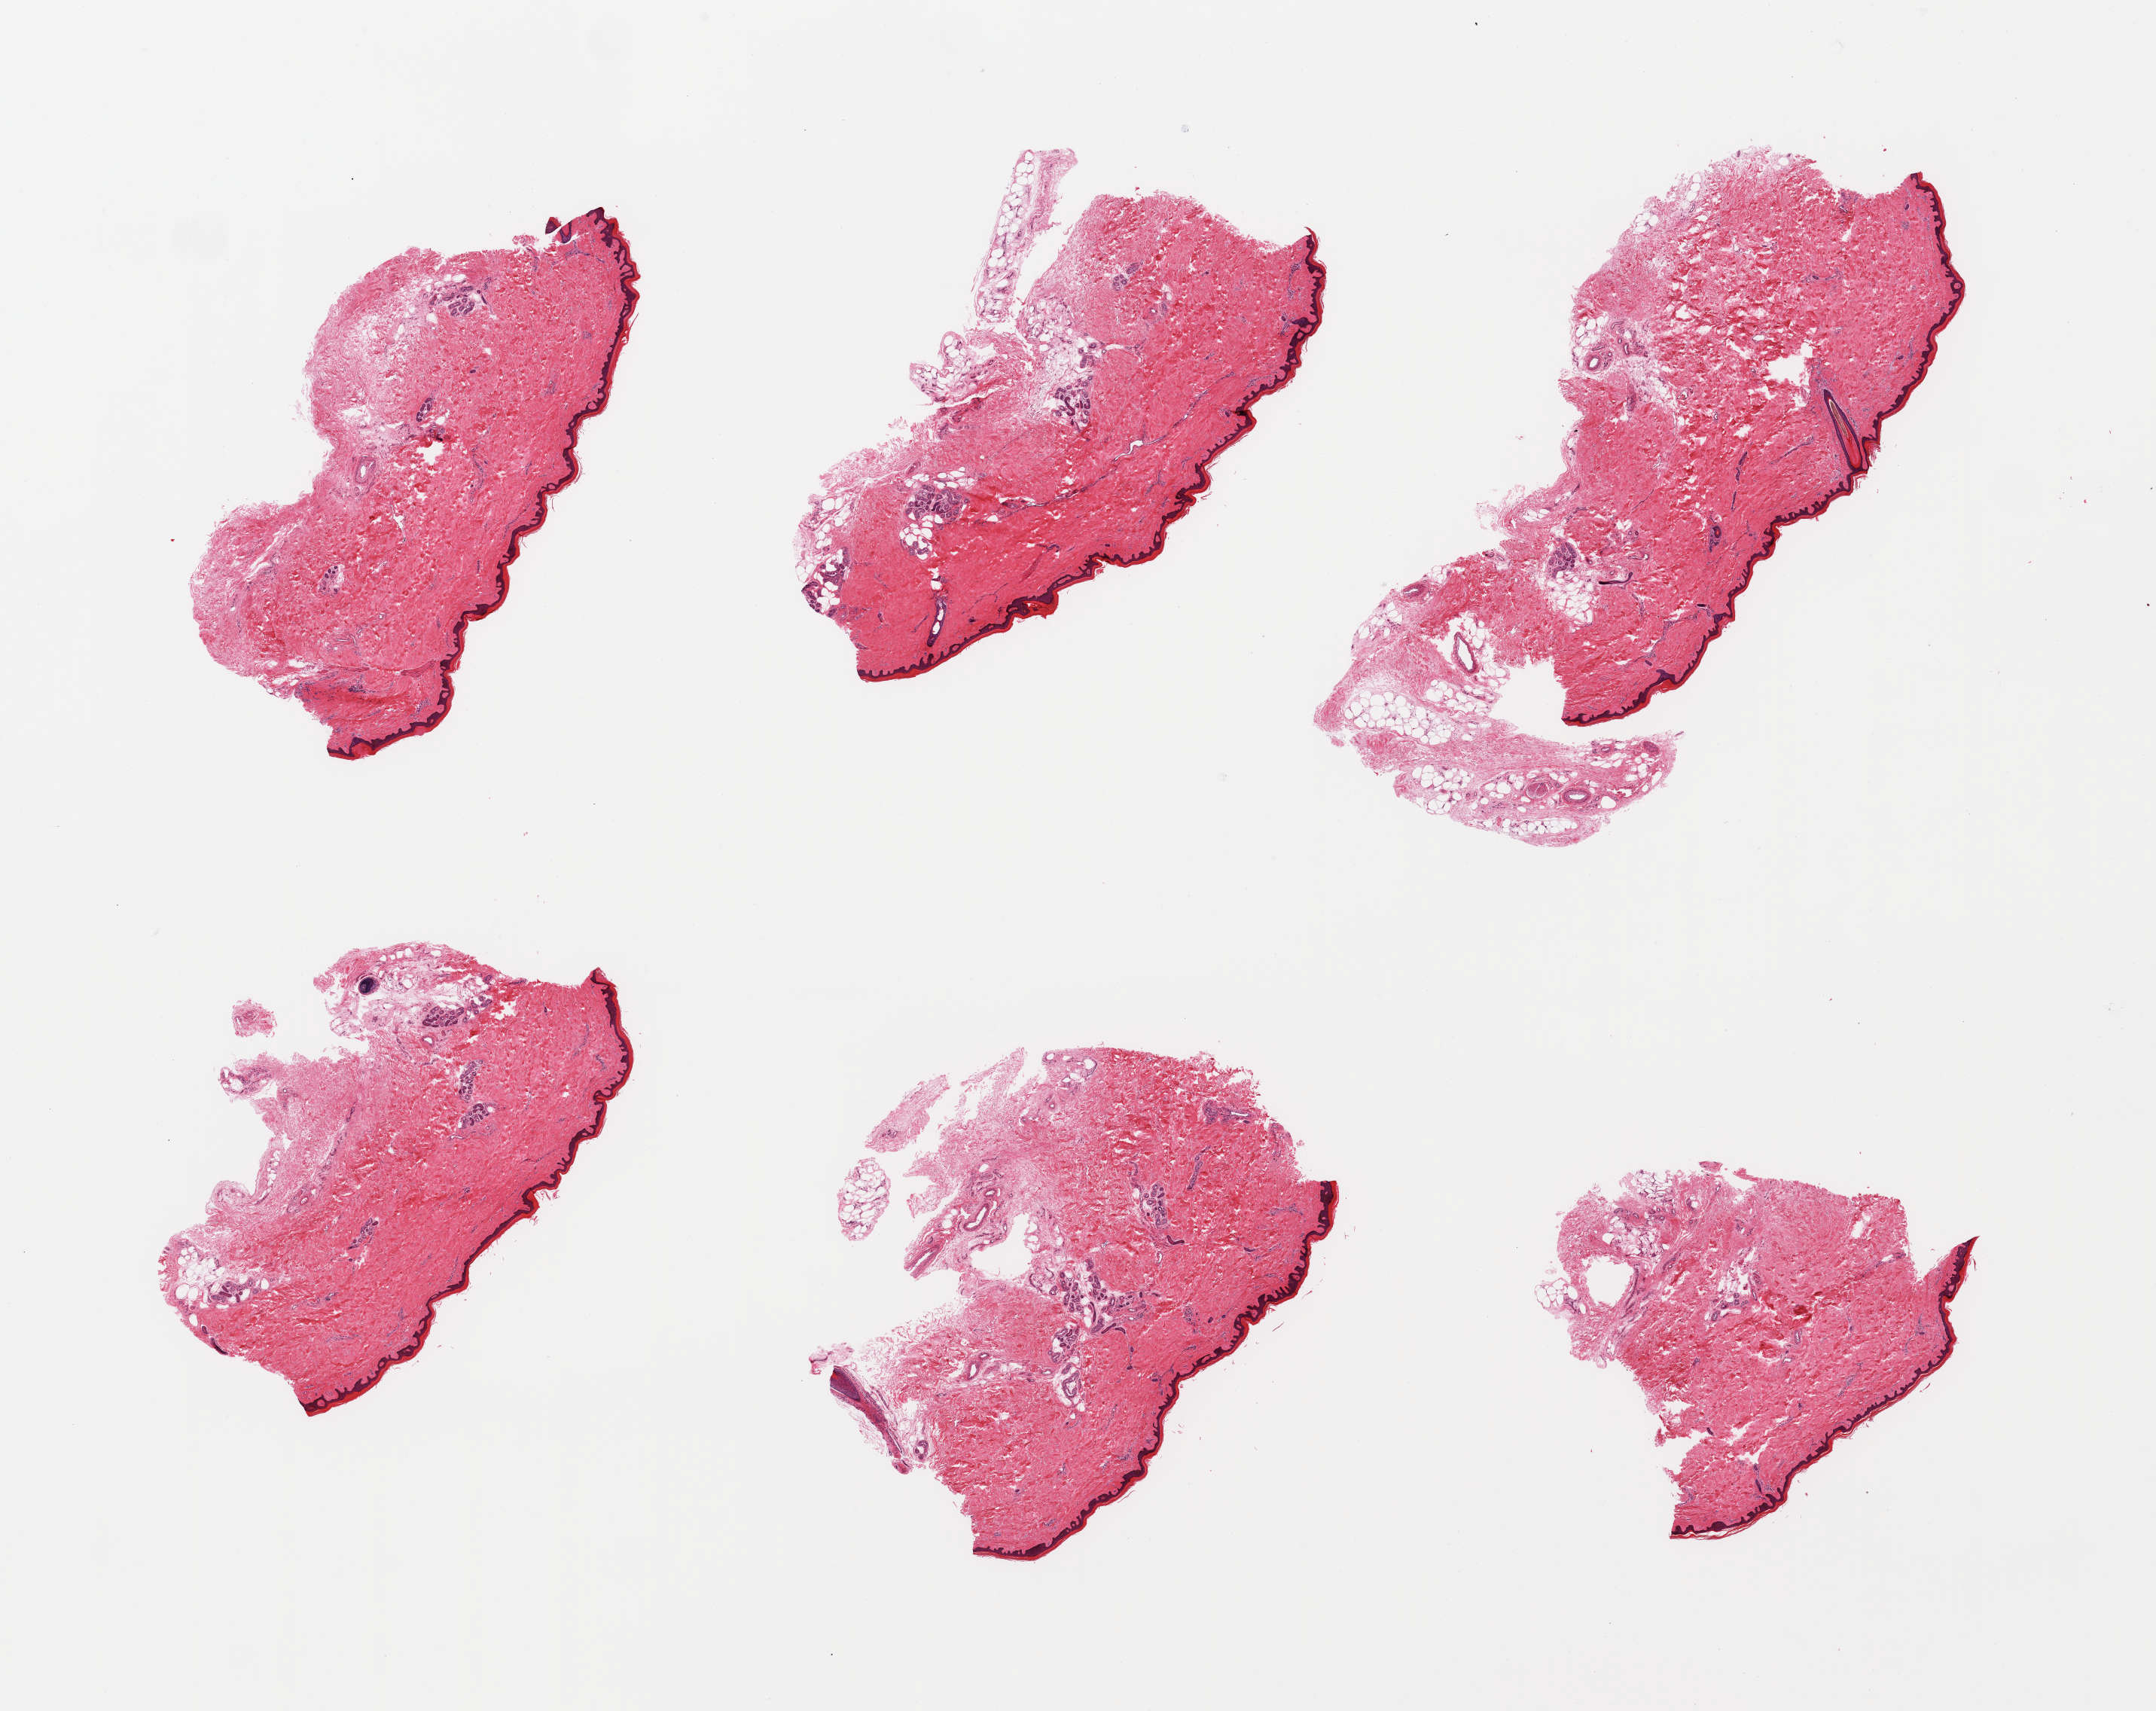
Whole-slide image, hematoxylin and eosin (H&E) stain, brightfield, a low-resolution overview of the entire scanned area, about 22.6 x 18.0 mm, PAXgene-fixed paraffin-embedded (PFPE) section, section of skin of lower leg (target tissue), tissue donor sample. Female donor.
- reviewer comment on this tissue sample: 6 pieces, squamous epithelium is ~30-40 microns; tags of adherent dermal fat up to ~0.3mm